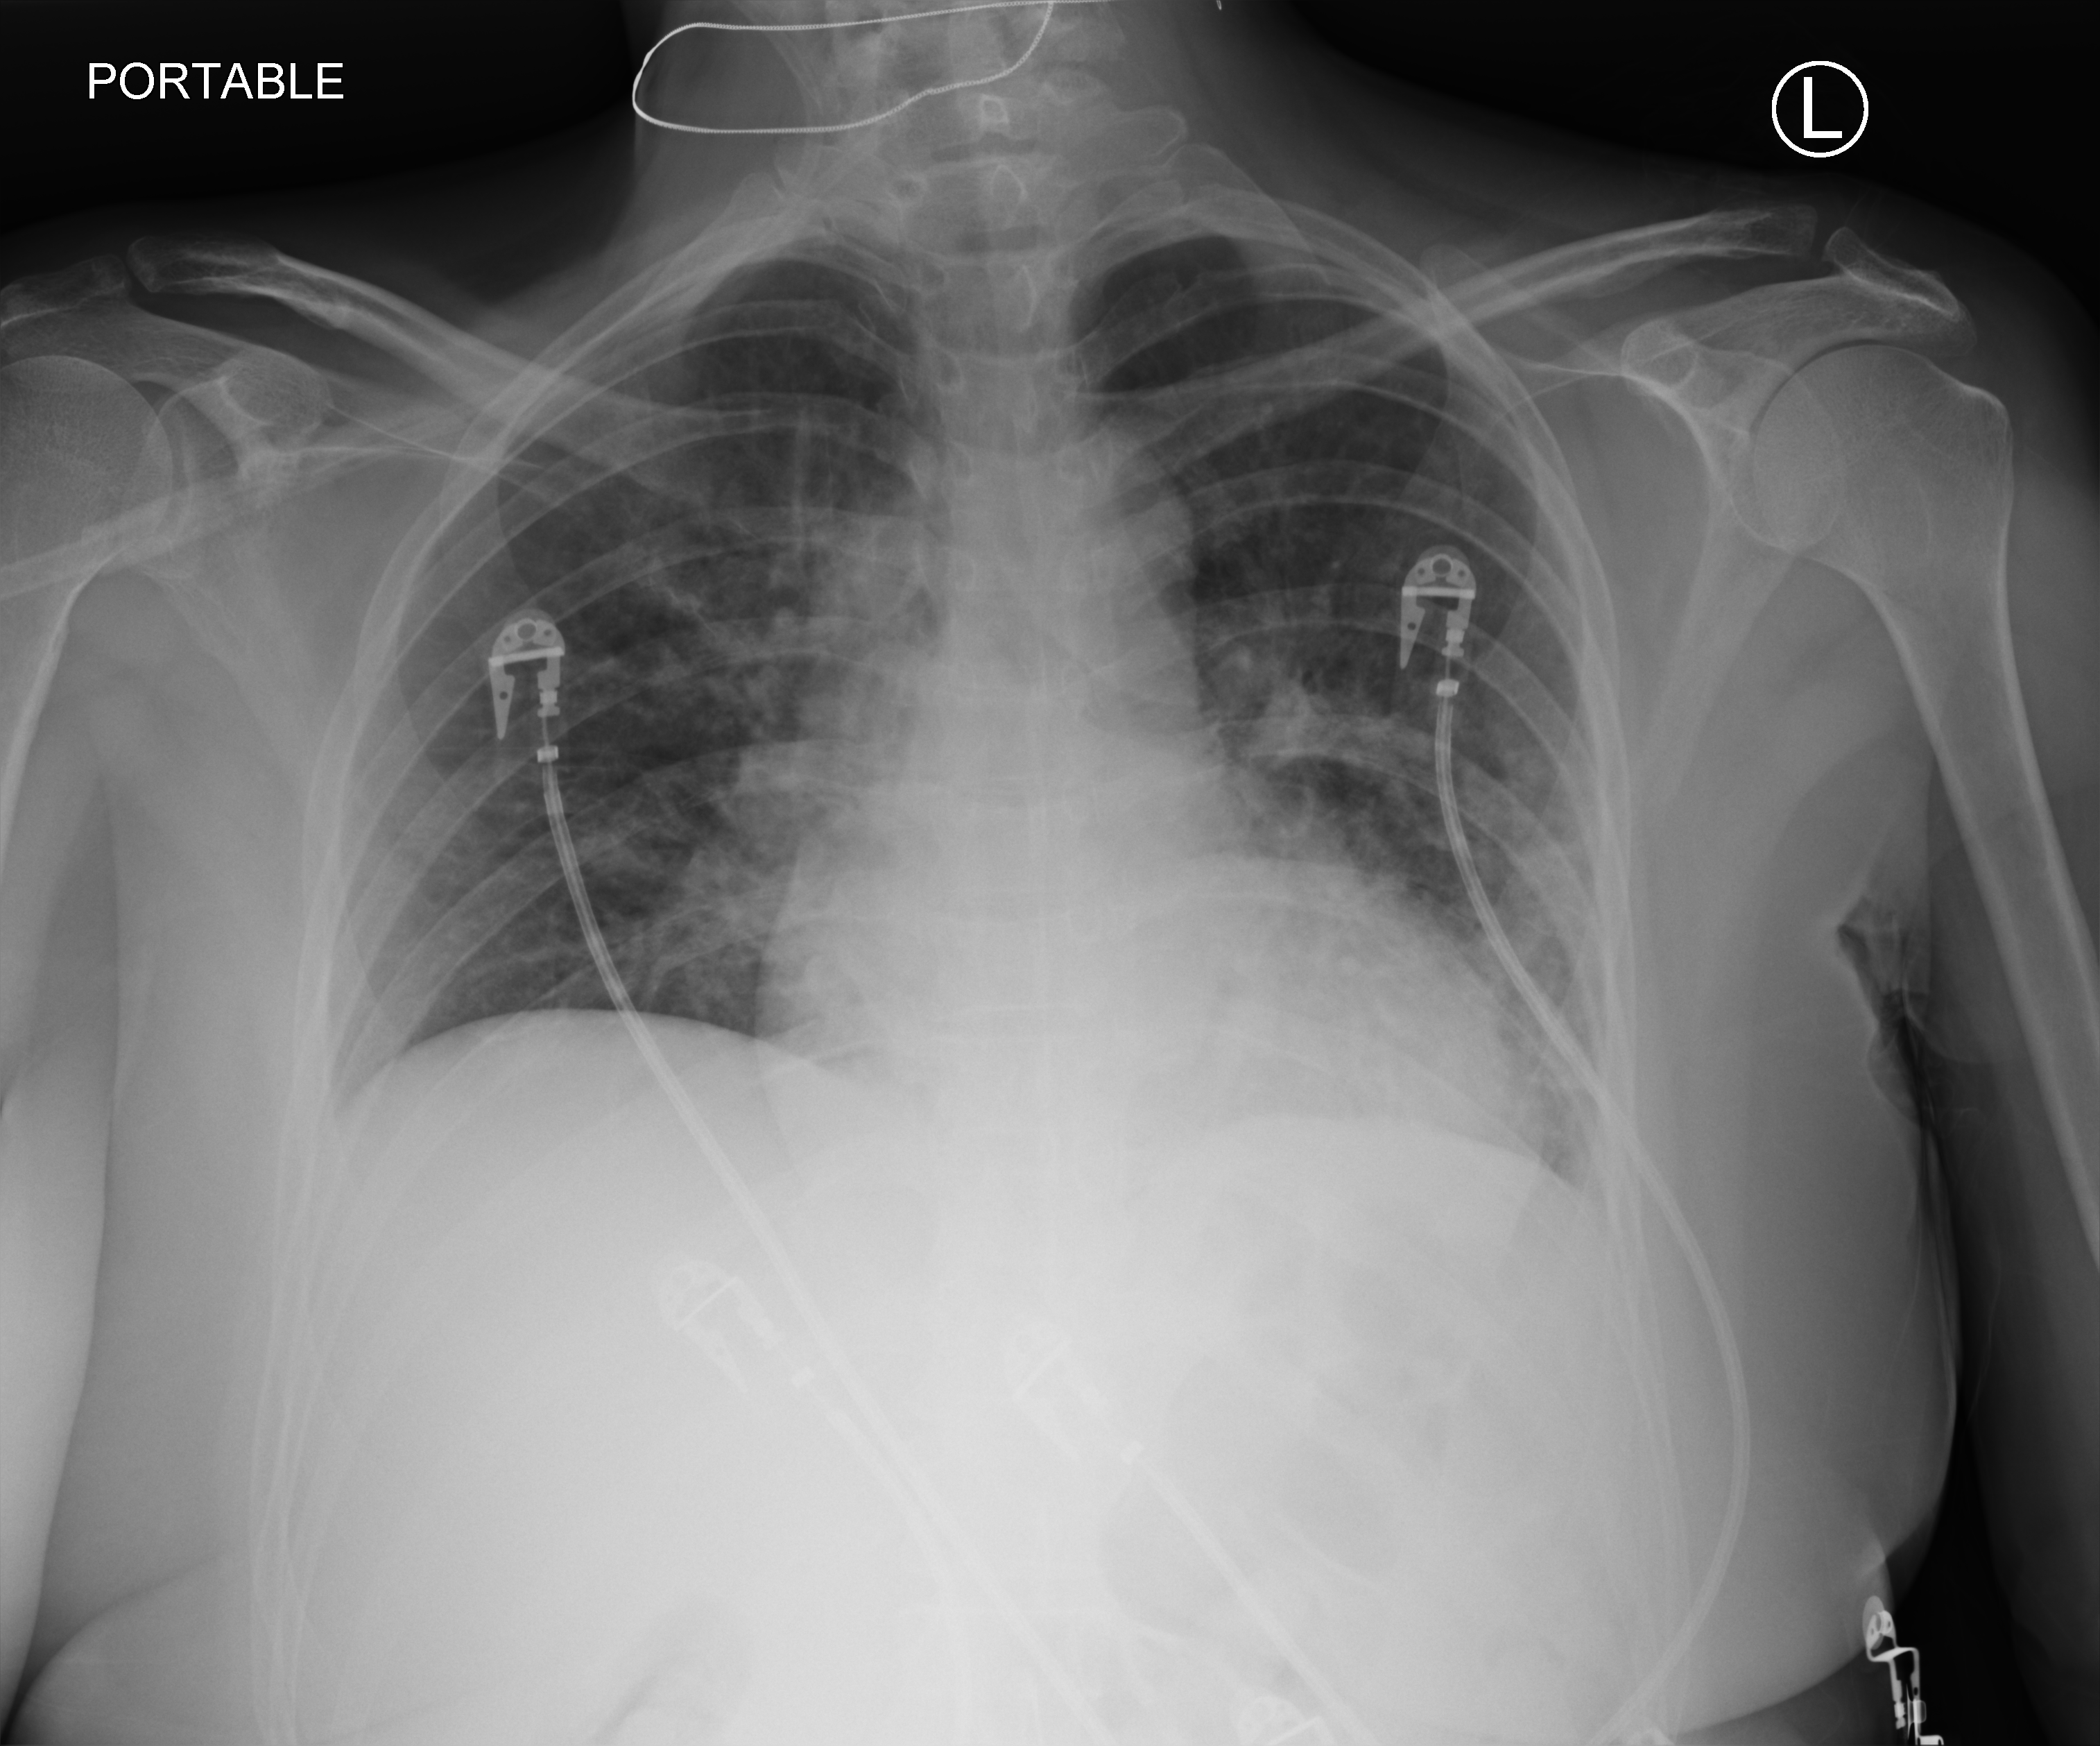
Bedside chest radiograph (computed radiography), anteroposterior (AP) projection. Female patient hospitalised with COVID-19, age 18–59 years.
Admission-level facts for this patient (not findings on this image; timing relative to this image not recorded): other chronic lung disease (admission record): no; mechanically ventilated during this hospital stay: no.